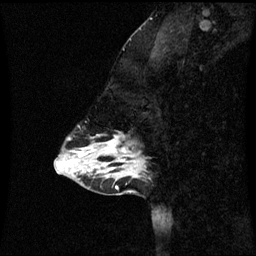
Breast MRI (dynamic contrast-enhanced), one sagittal slice; slice 18 of 60 in the series (ordered by position); dynamic contrast-enhanced series, image 2 of 3 at this slice position (ordered by acquisition); 1.5 T; TE 4.2 ms, TR 8.9 ms; 2 mm slice thickness; 256 × 256 image matrix, field of view 220 × 220 mm. Female patient, age 43 years. Case-level facts recorded for this patient, not image findings: setting: breast cancer imaged before/during neoadjuvant chemotherapy; receptor status: HR-positive, HER2-negative.
Structures marked on this image (semi-automatic segmentation, software-assisted and operator-edited):
- analysis volume of interest (the breast-tissue region the enhancement analysis was run in; not a lesion): box from (x=84, y=136) to (x=144, y=171) px
- tumour enhancement mask (voxels above the 70 % enhancement threshold inside the analysis volume of interest): (x=105, y=140)–(x=125, y=163)